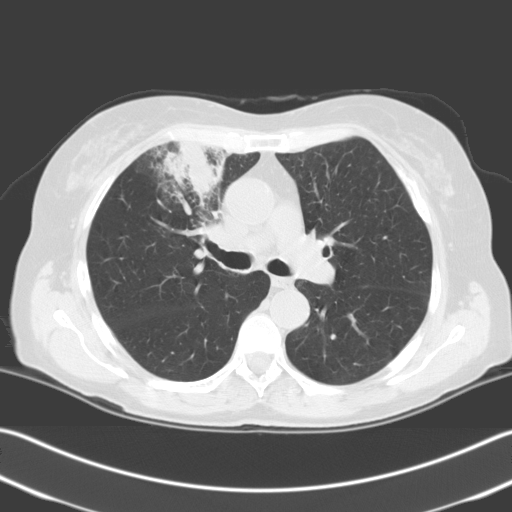
Low-dose screening chest CT, one axial slice. Position 136 of 204 along the scan axis. 140 kVp. Lung window (W 1500 / L -600 HU). 512 × 512 image matrix, field of view 348 × 348 mm.
Annotated regions visible in this slice (outlined manually by an expert reader):
- lesion 1 (tumor, upper lobe of right lung): bounding box [x1, y1, x2, y2] px = [163, 142, 229, 206]